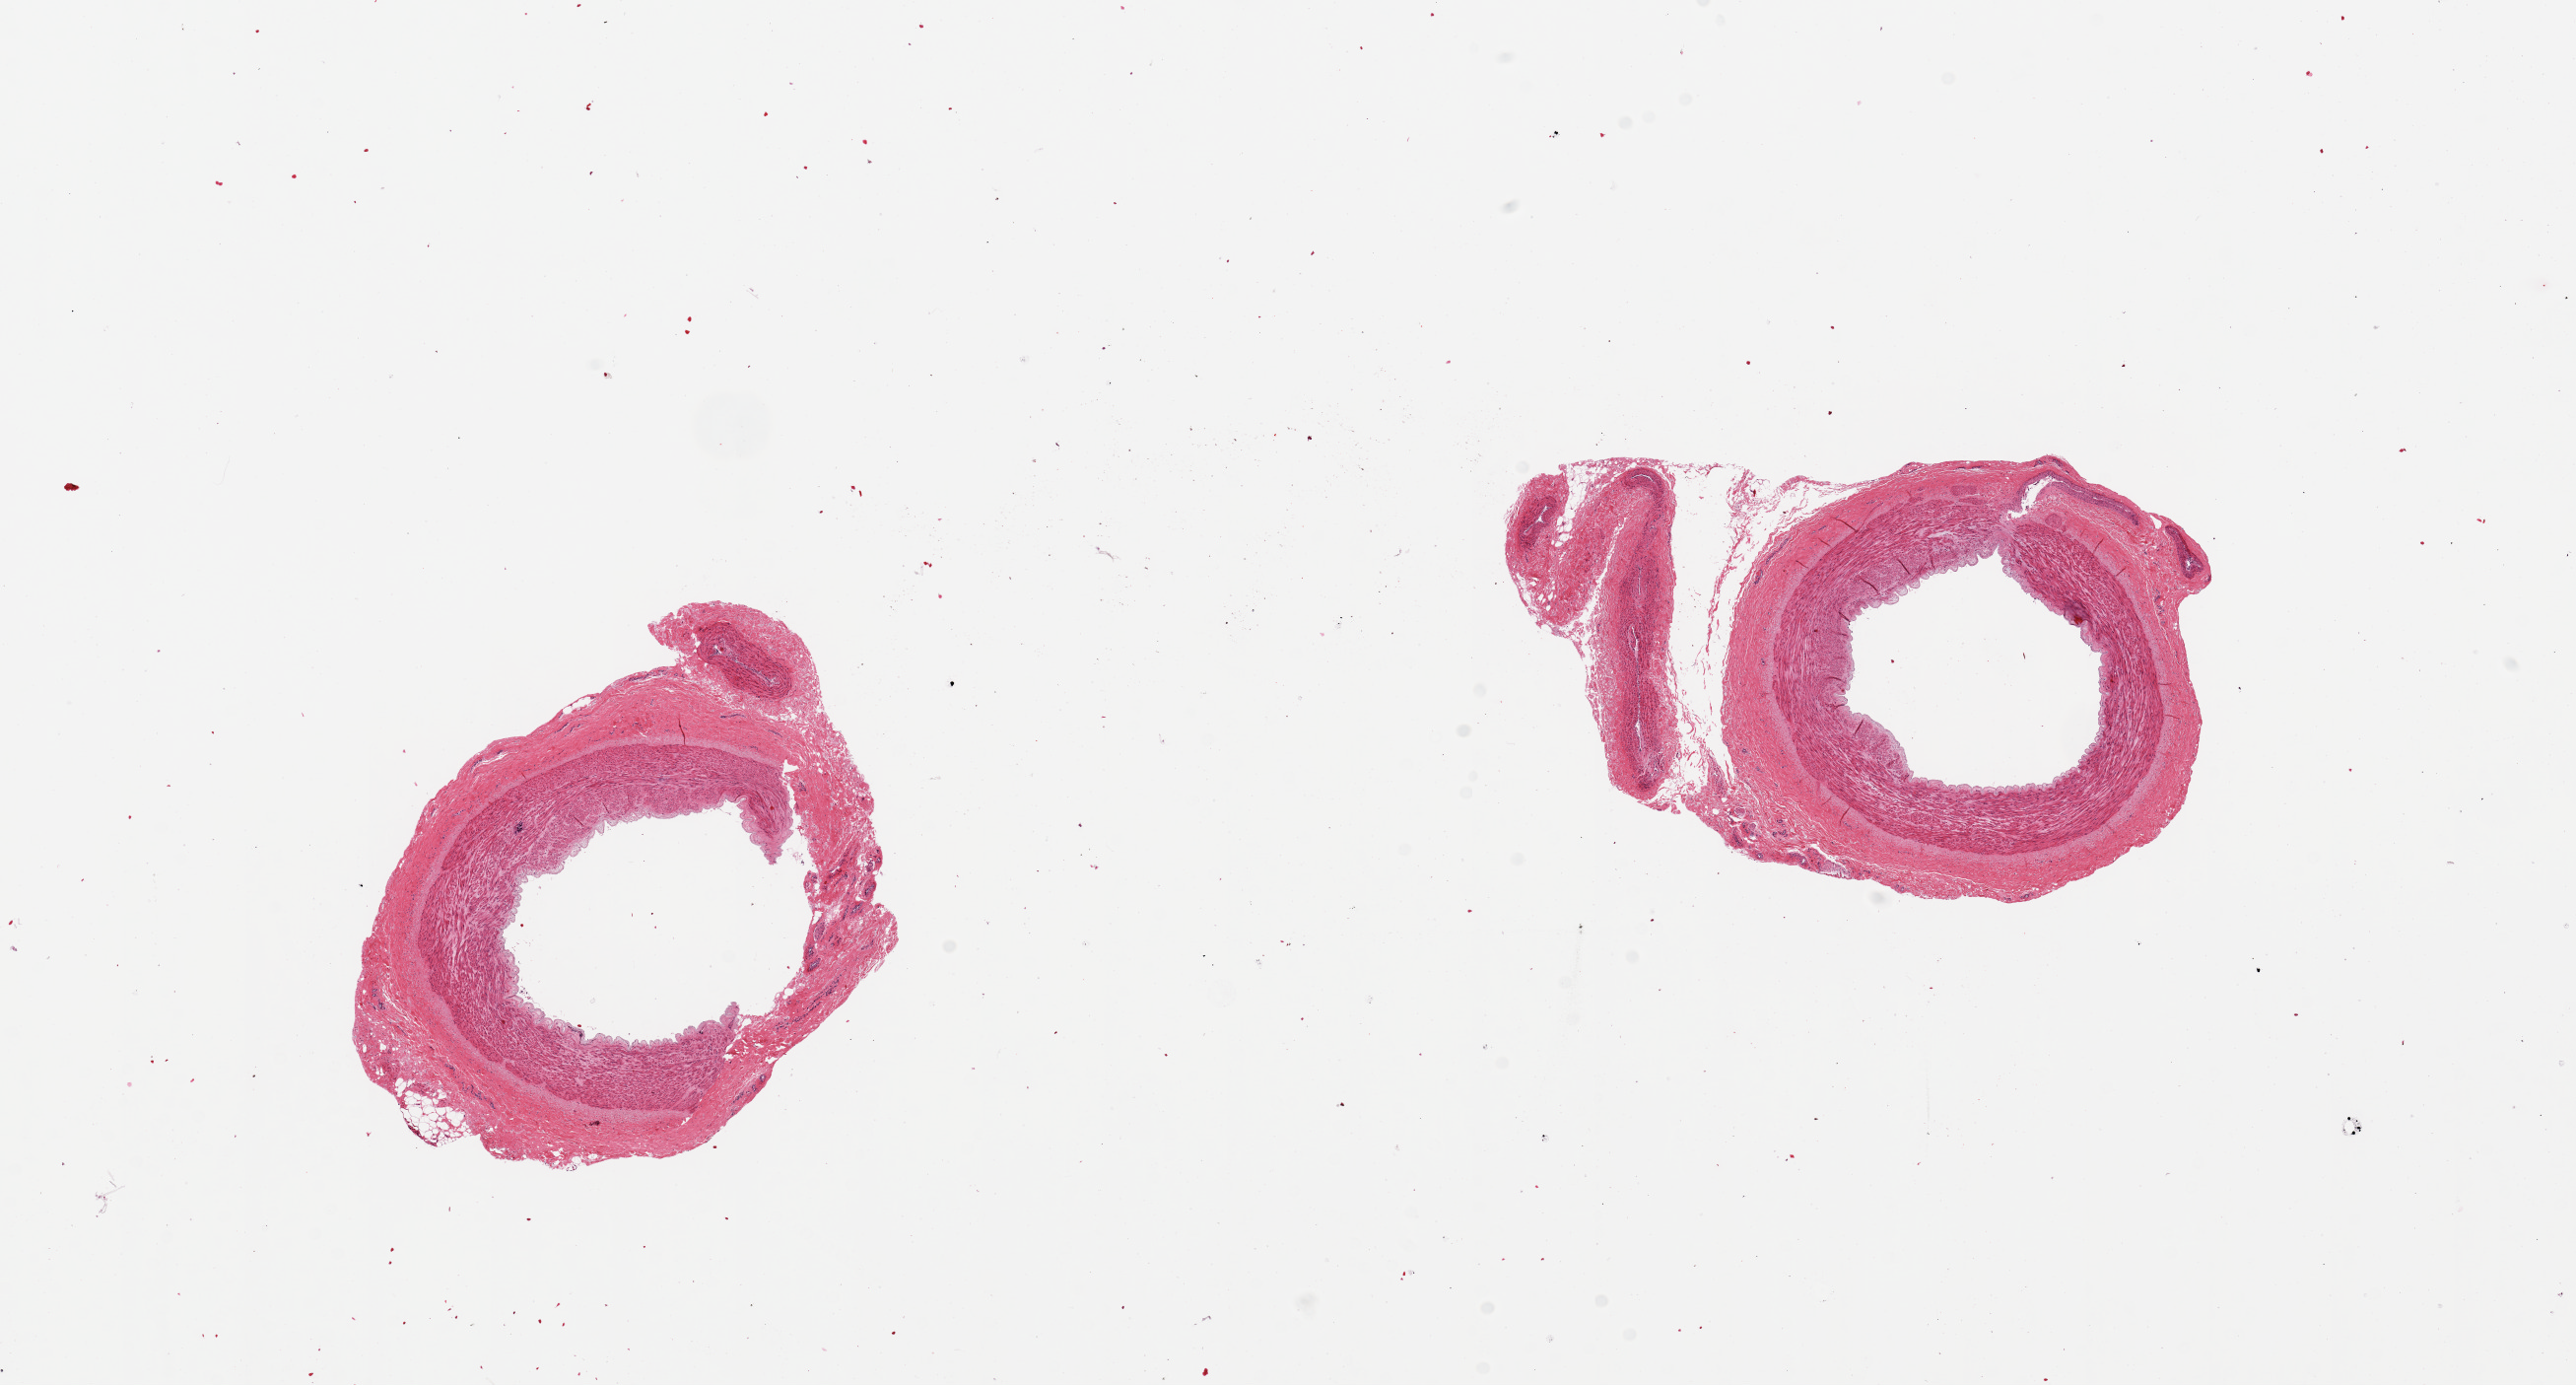
H&E whole-slide image, whole scanned area (about 20.7 x 11.1 mm) shown as a low-resolution overview, PAXgene-fixed paraffin-embedded (PFPE) section, sampled site (target tissue): tibial artery, tissue donor sample. Donor sex: female.
Review note (as recorded): 2 pieces, few small foci of calcification within wall, both with attachment of fibrofatty tissue.